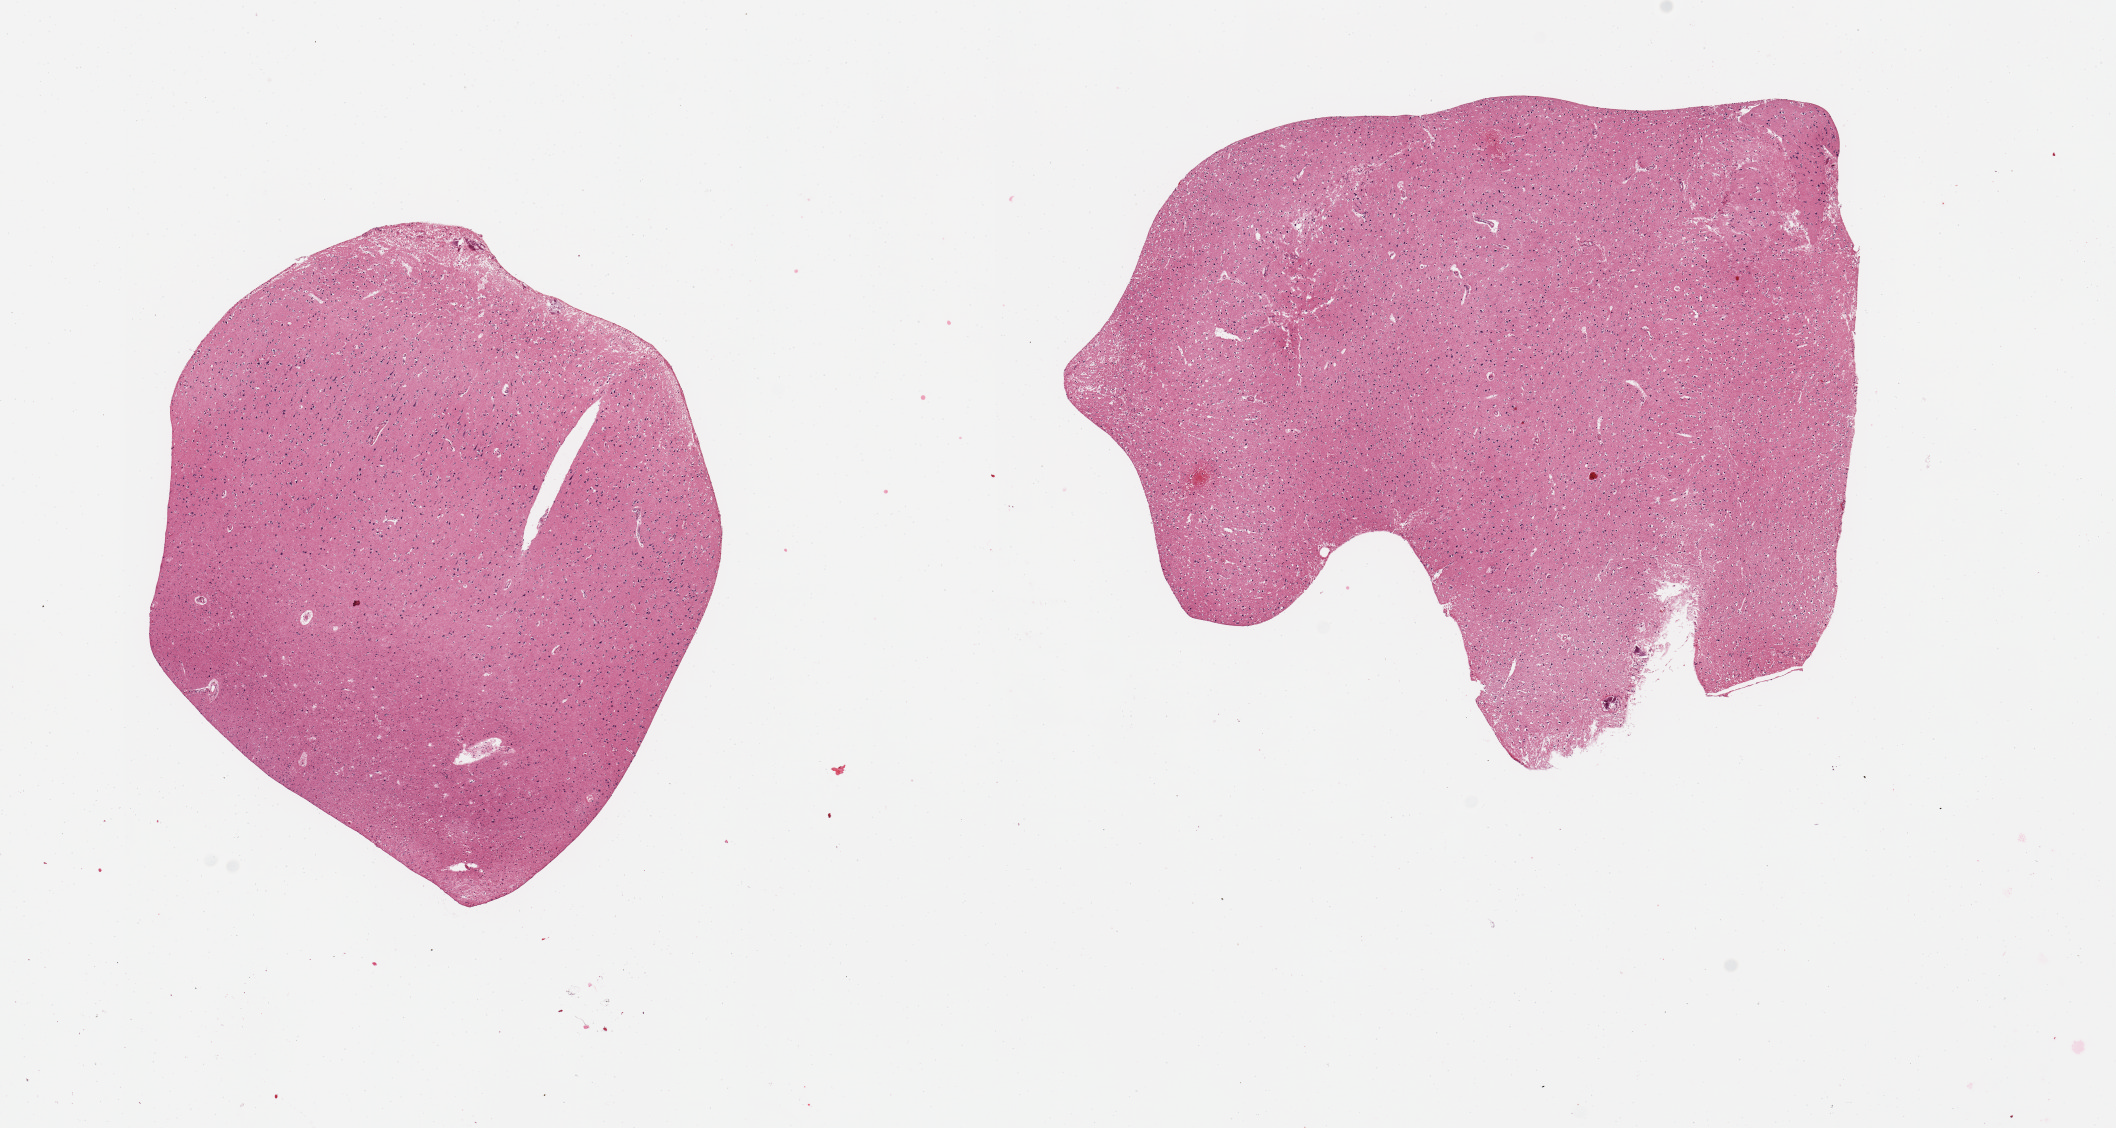
H&E whole-slide image, whole scanned area (about 16.7 x 8.9 mm, acquisition: 20x scan) shown as a low-resolution overview, PAXgene-fixed, paraffin-embedded tissue, section of cerebral cortex (target tissue), donor tissue sample.
• pathologist's review note for this sample: 2 pieces